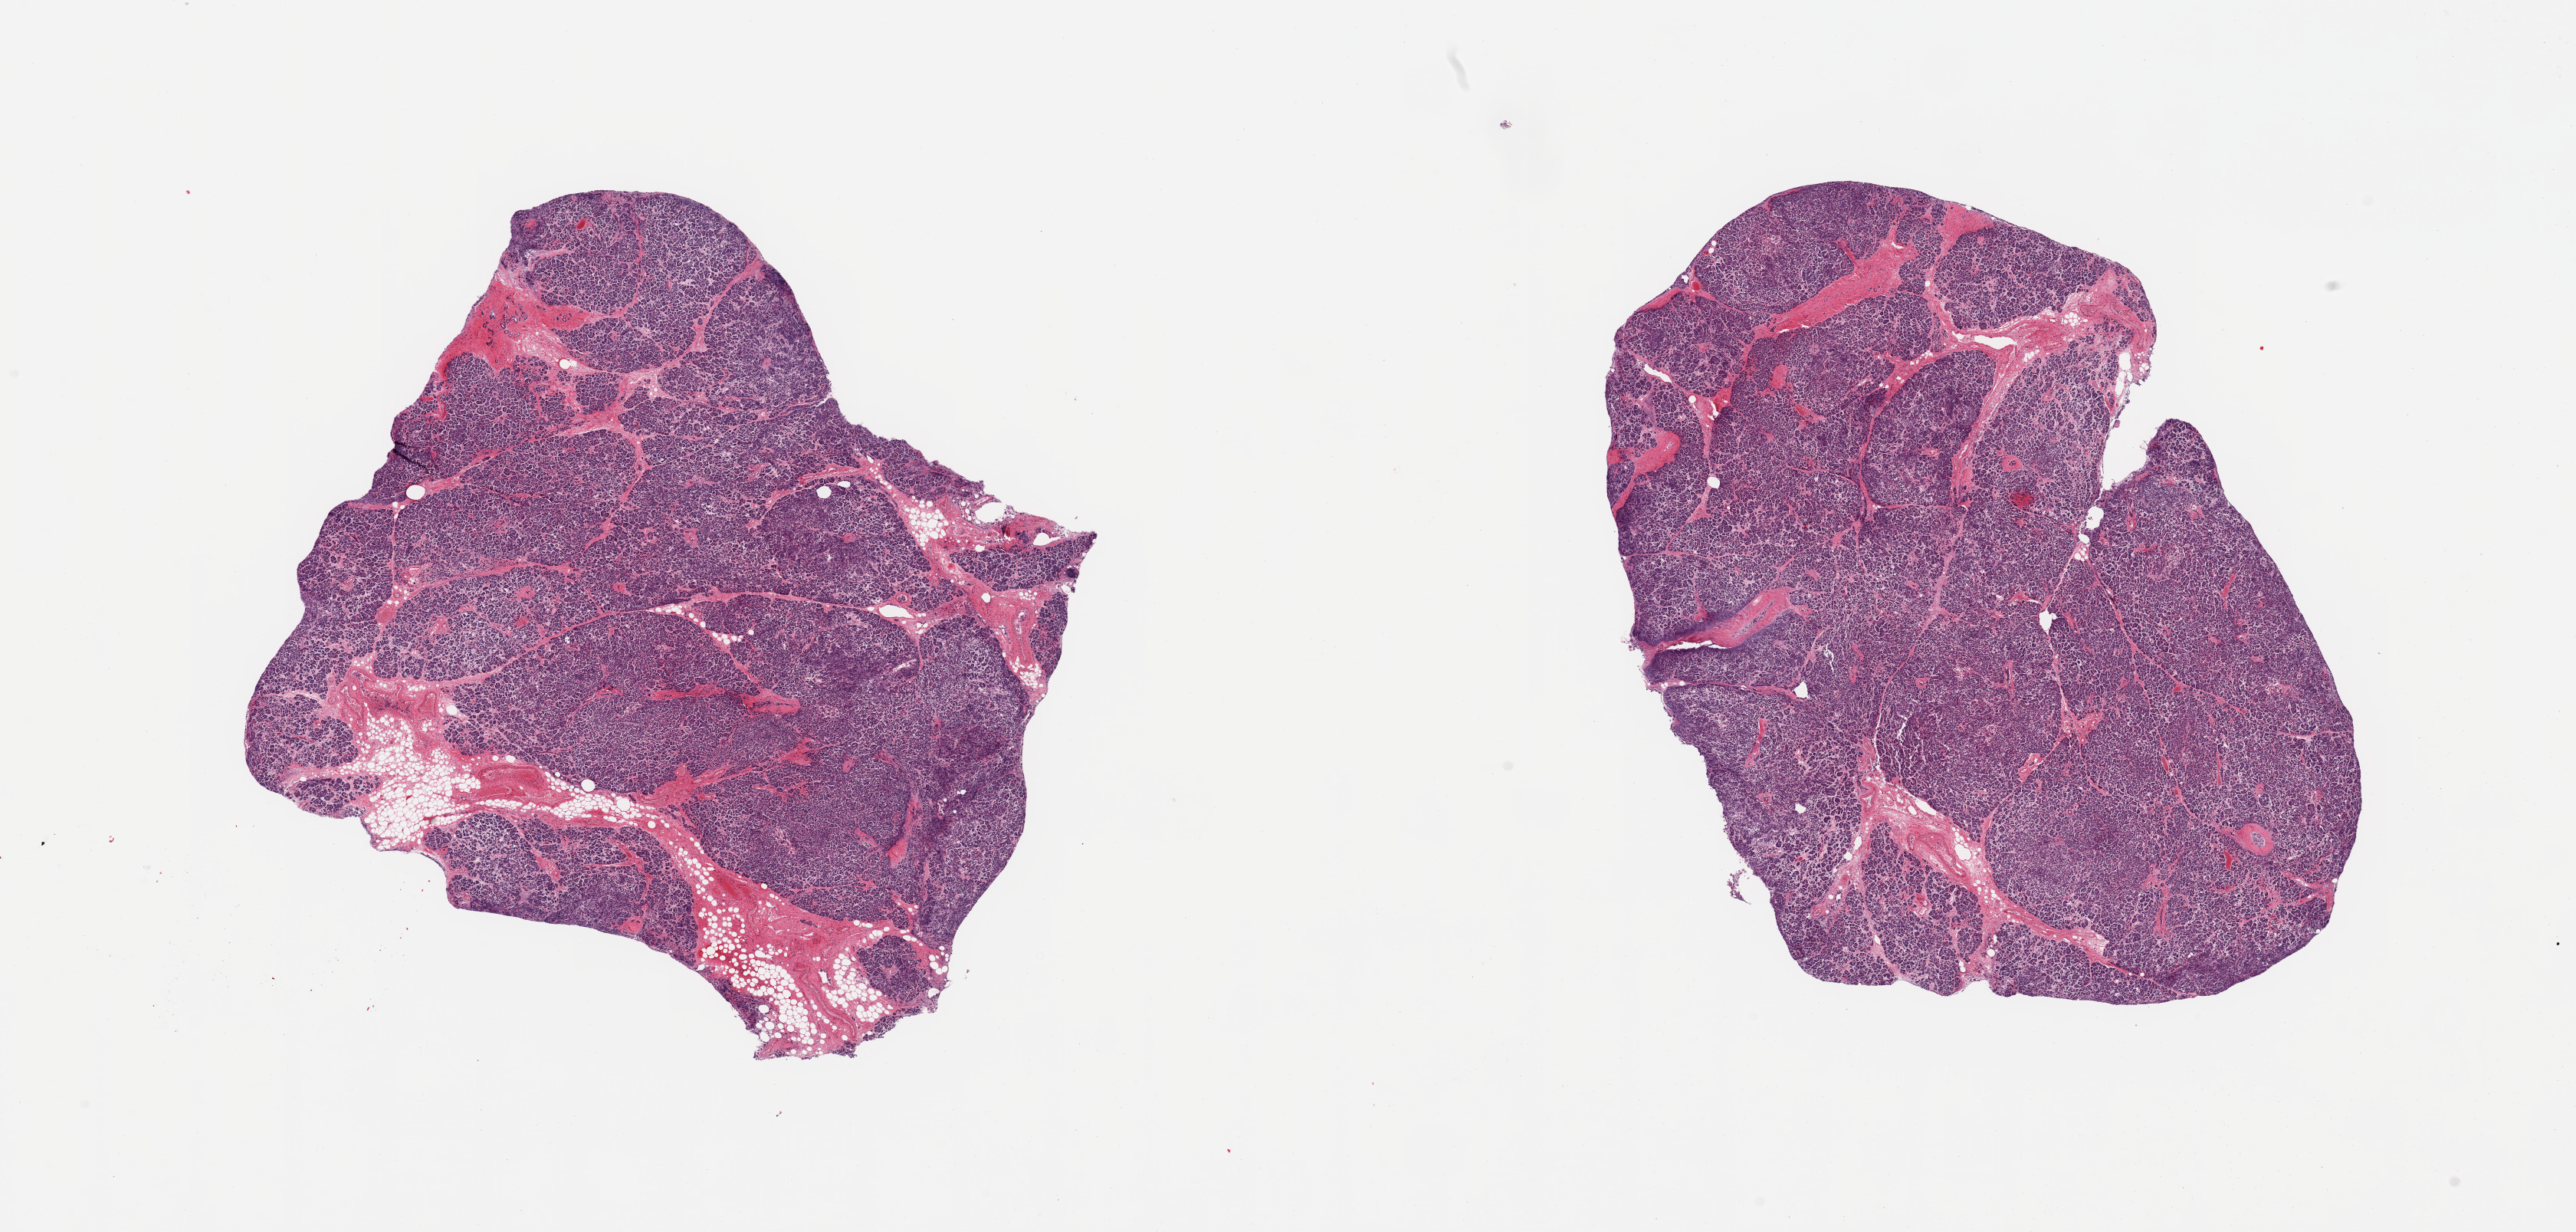
Digitized H&E-stained section, a low-resolution overview of the entire scanned area, about 26.6 x 12.7 mm, PAXgene-fixed, paraffin-embedded tissue, target tissue: pancreas, donor tissue sample. Donor: male.
Review note (as recorded): 2 pieces; 10% internal fat in 1 piece.